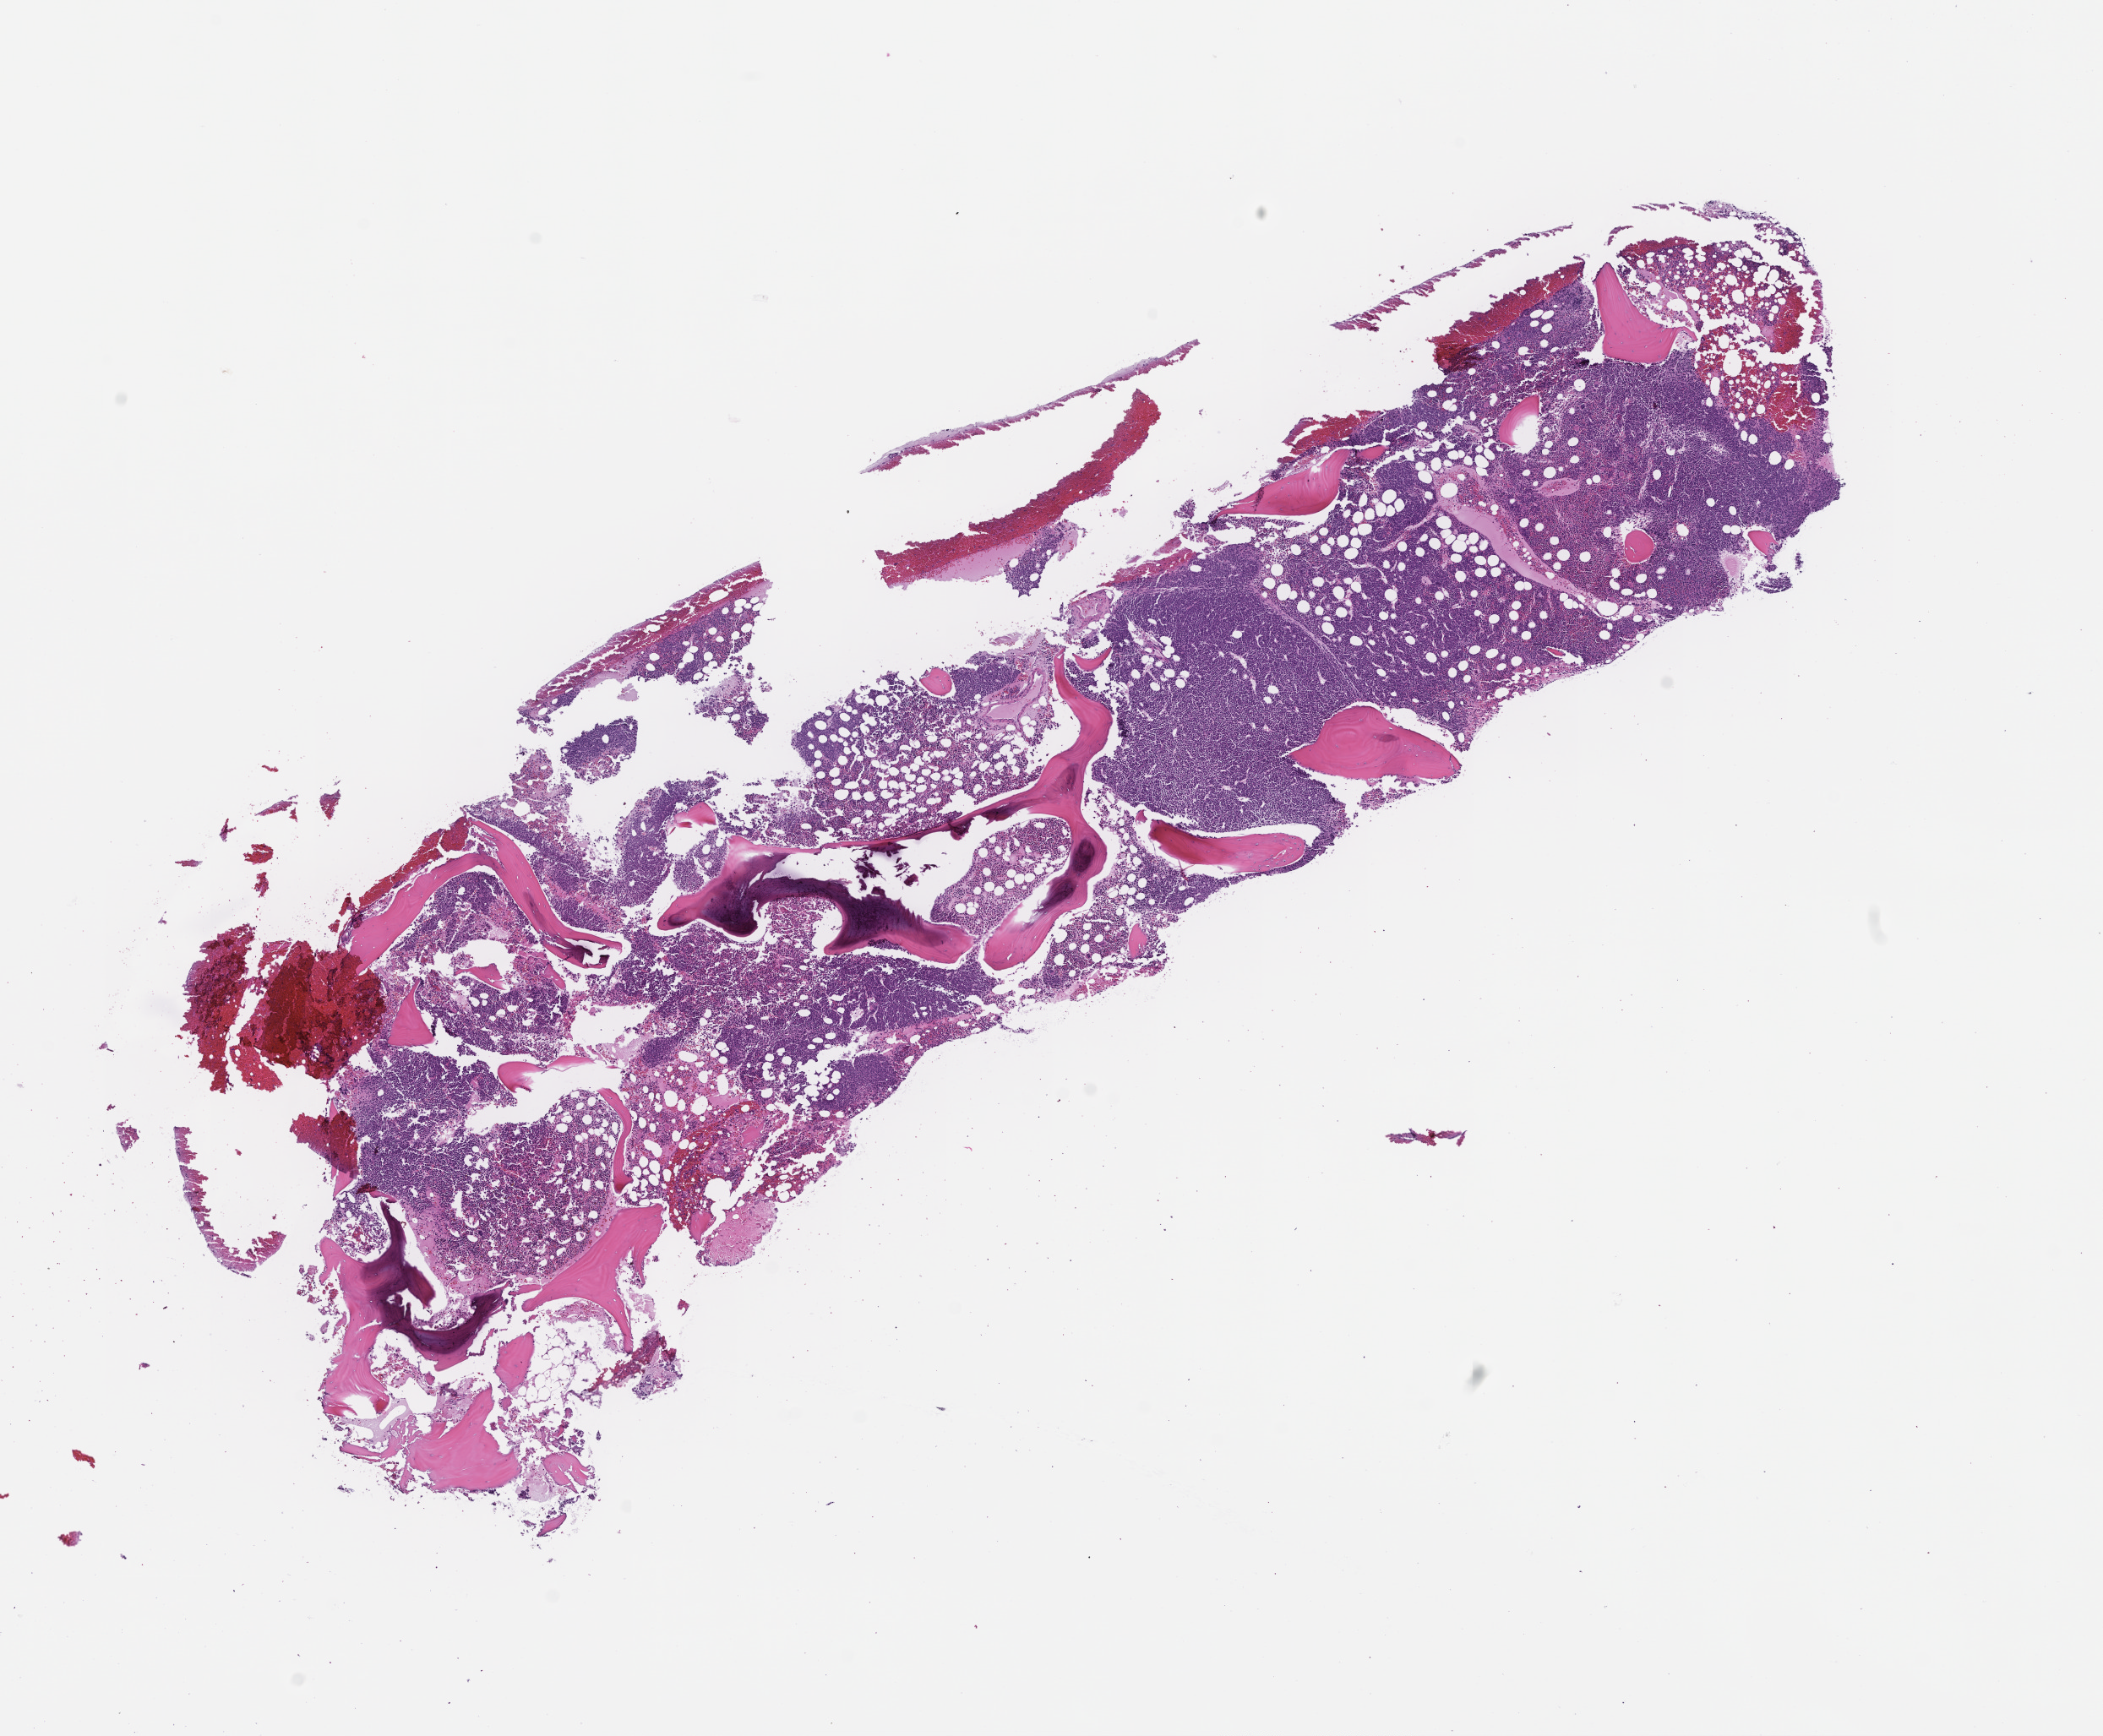
Whole-slide image, haematoxylin and eosin stain — shown as a low-resolution overview of the whole scanned area (about 10.1 x 8.3 mm). FFPE section. Site: bone marrow. Archival tissue. Female patient.
* this section: primary tumor
* diagnosis: Plasma Cell Myeloma